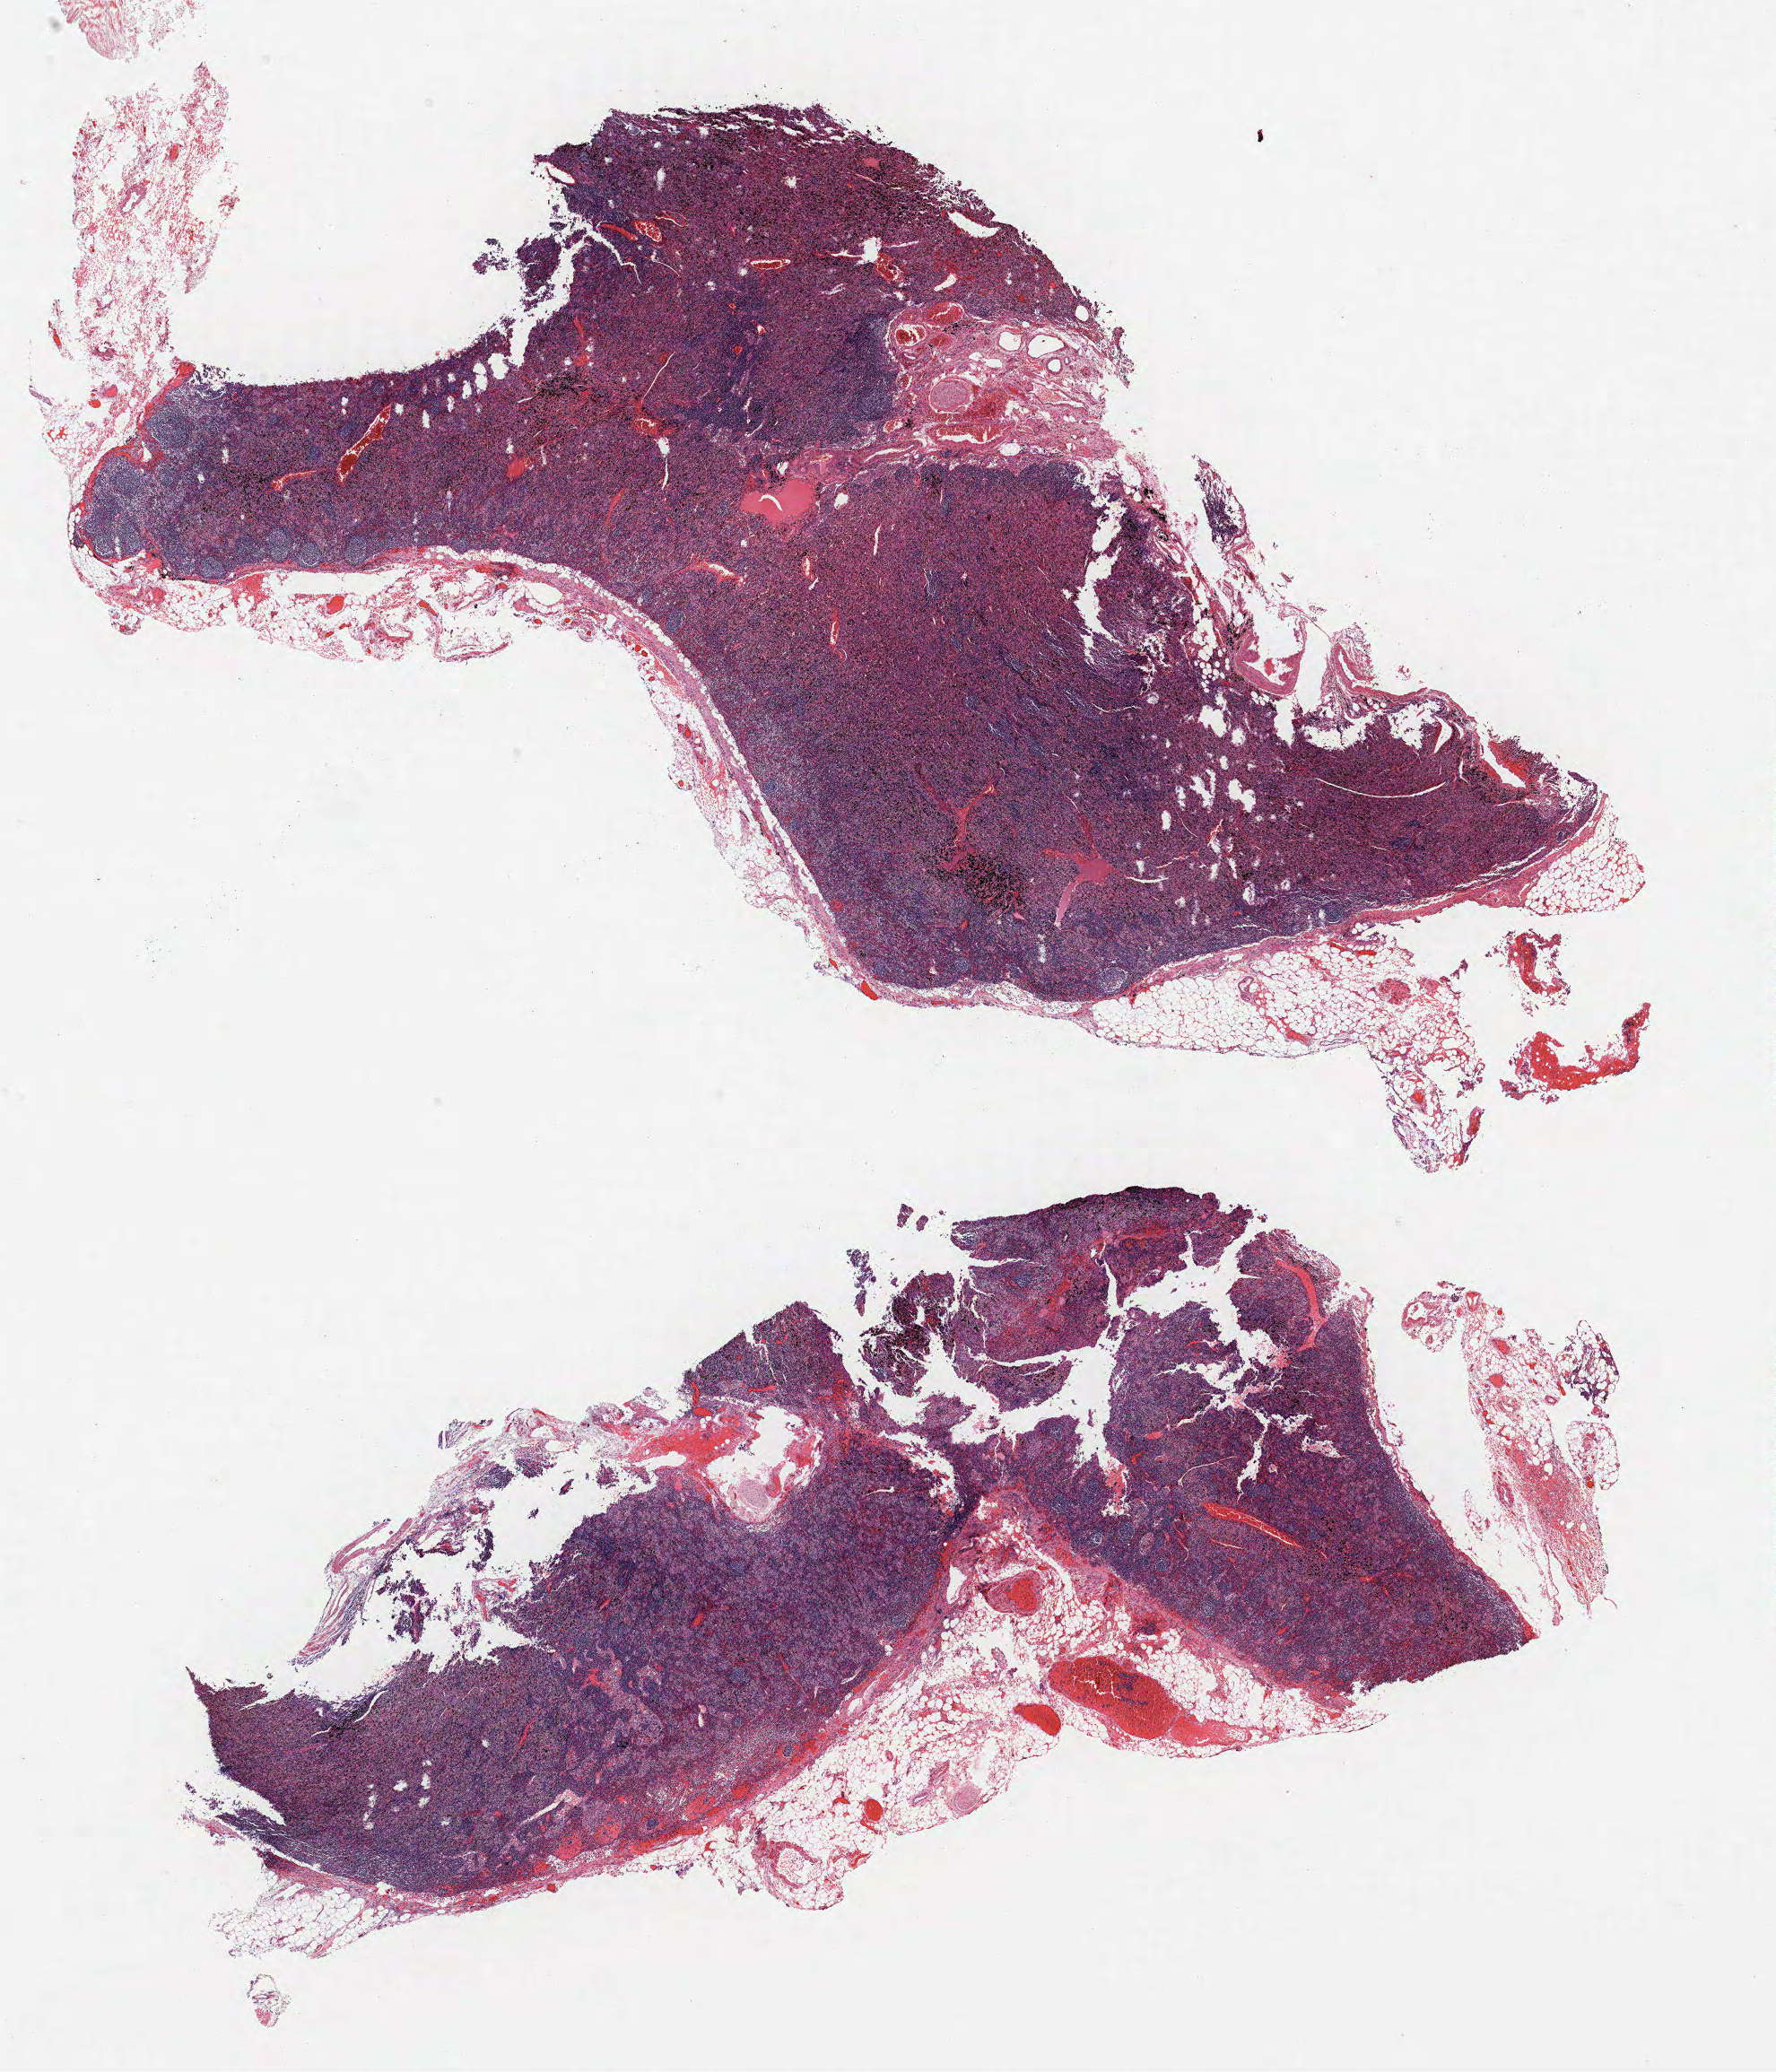
Whole-slide histology image, H&E-stained, whole scanned area (about 15.8 x 18.5 mm, from a 40x scan) shown as a low-resolution overview; FFPE section; lung tissue. Male, age 66 at enrolment. Former smoker at enrolment. Grade: moderately differentiated (G2).
• participant's lung-cancer diagnosis: Adenocarcinoma, NOS (ICD-O-3 8140/3)
• ICD-O-3 topography: upper lobe of lung (C34.1)
• primary tumour location (clinical record): left upper lobe
• tumour size (pathology): 9 mm
• stage (AJCC 6th edition): IIB